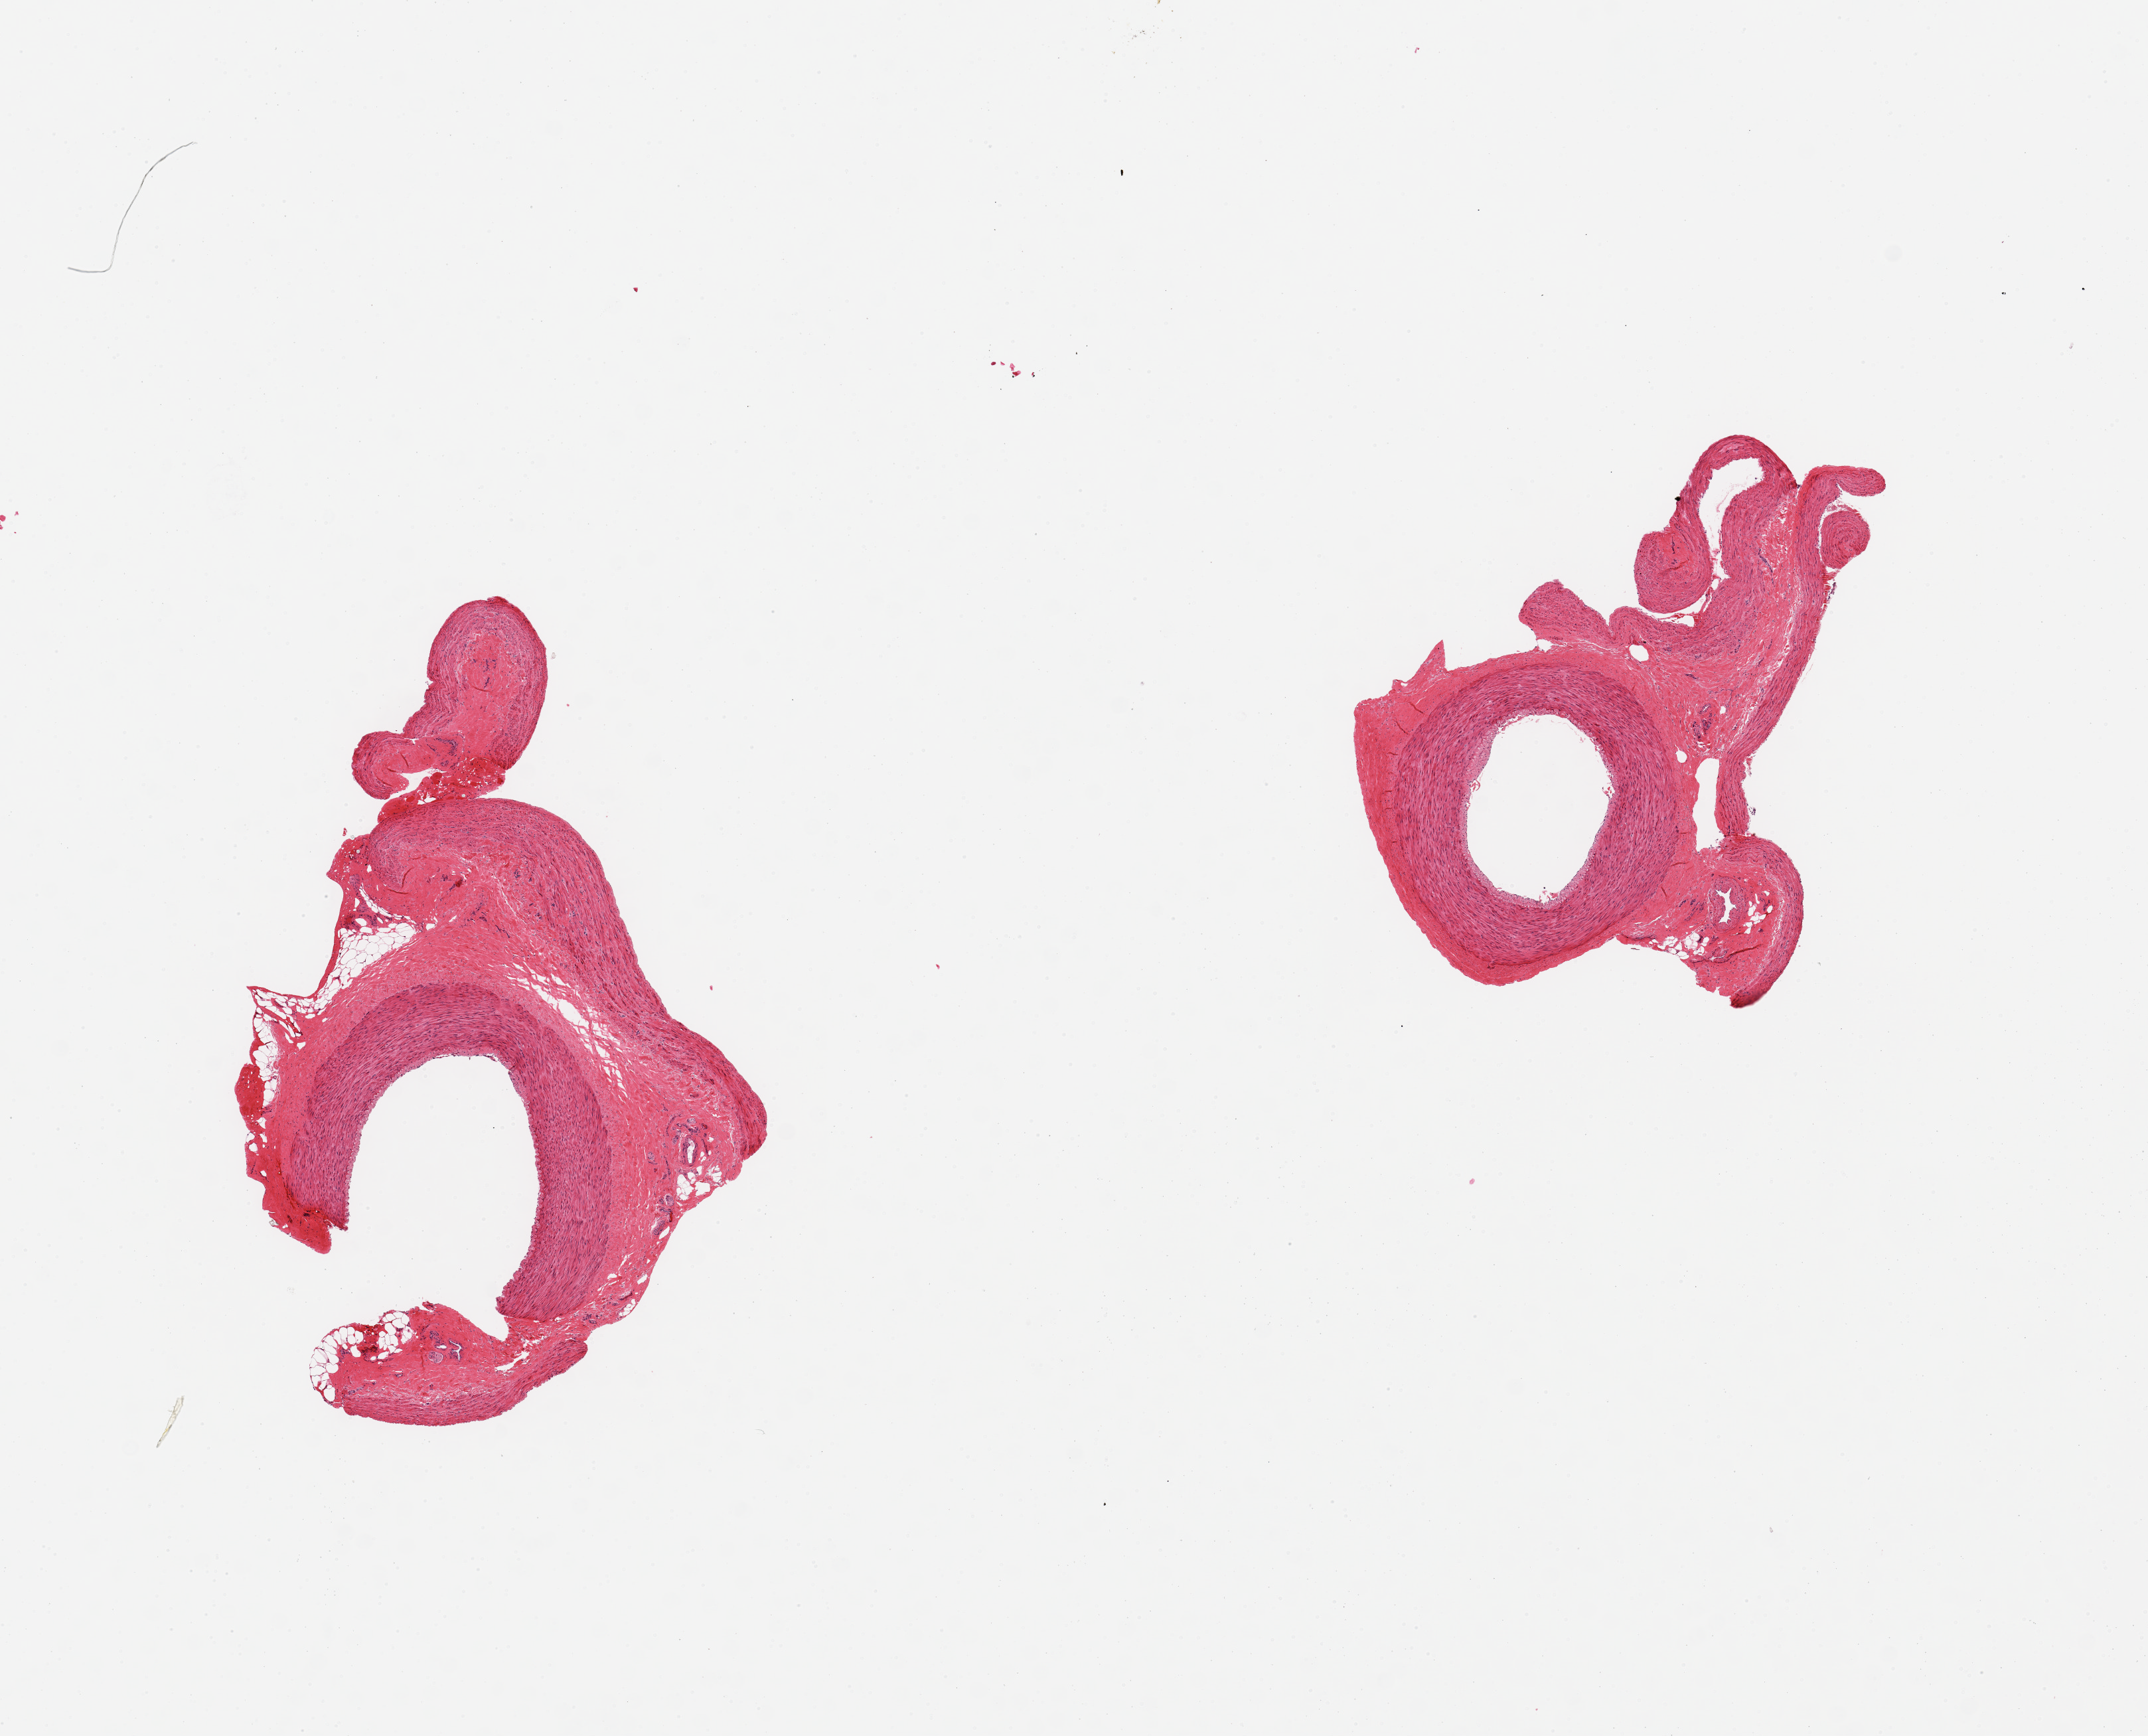
H&E whole-slide image — low-resolution overview of the scanned area, about 12.8 x 10.3 mm (acquisition: 20x scan). PAXgene-fixed, paraffin-embedded tissue. Target tissue: tibial artery. Tissue donor sample. Male donor.
* review note (as recorded): 2 pieces; well trimmed, no lesions